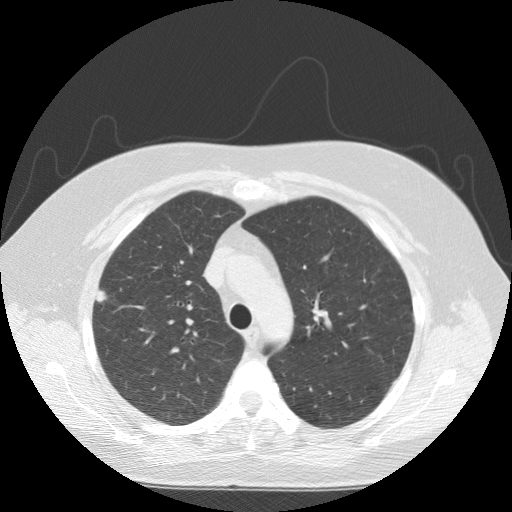
Low-dose screening chest CT, one axial slice; slice 109 of 146 in the series (ordered by position); reconstruction kernel STANDARD; 120 kVp; lung window (W 1500 / L -600 HU); 2.5 mm slice thickness; 512 × 512 image matrix.
Structures marked on this image (manually delineated by an expert):
- lesion 1 (tumor, upper lobe of right lung): bounding box [x1, y1, x2, y2] px = [96, 290, 106, 302]